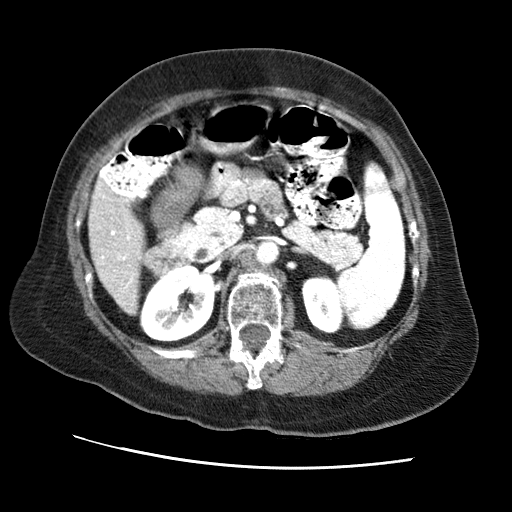
Contrast-enhanced abdominal CT (liver protocol), one axial slice. Slice 22 of 65 in the series (ordered by position). 120 kVp. Soft-tissue window (W 400 / L 40 HU). 512 × 512 image matrix, field of view 340 × 340 mm. From the clinical record (not read from this slice): diagnosis: hepatocellular carcinoma (patient treated with transarterial chemoembolisation; whether this scan precedes or follows treatment is not stated here); TNM stage (as recorded): Stage-II; Child-Pugh class: A; tumour differentiation: no biopsy; tumour nodularity: multinodular.
Annotated regions visible in this slice (semi-automatic segmentation, software-assisted and operator-edited):
- liver parenchyma outside the tumour (the mass and vessels are separate outlines, so this box may not span the whole liver): bounding box [x1, y1, x2, y2] px = [88, 182, 142, 314]
- liver vessels: [98, 187, 134, 289]